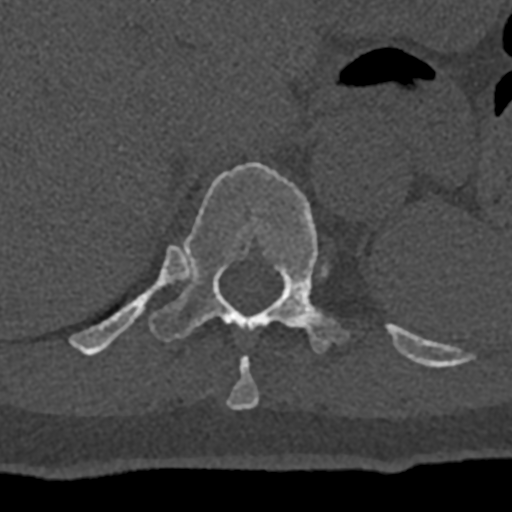
CT including the spine, one axial slice. Position 554 of 797 along the scan axis. 120 kVp. Bone window (W 1800 / L 400 HU). 0.5 mm slice thickness. 512 × 512 image matrix, field of view 160 × 160 mm. Patient: male, 74 years. Case-level facts recorded for this patient, not image findings: primary cancer: renal; vertebrae with lytic lesions (as recorded): T10, L1, L2, L3, L4, L5.
Outlined on this slice (semi-automatically segmented with operator editing):
- T10 vertebra: box from (x=226, y=356) to (x=259, y=409) px
- T11 vertebra: (x=70, y=162)–(x=432, y=367)